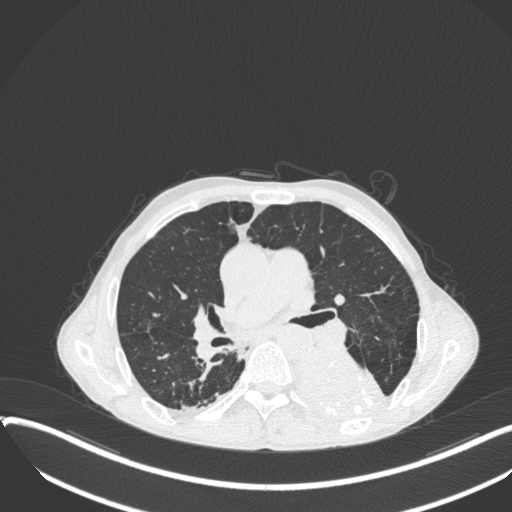
Chest CT, one axial slice; slice 215 of 400 in the series (ordered by position); reconstruction kernel B31f; lung window (W 1500 / L -600 HU); 1 mm slice thickness; 512 × 512 image matrix. Patient: male, 57 years. From the clinical record (not read from this slice): clinical TNM (as recorded): T4 N0 M0.
Structures marked on this image (rectangle marked by the reading radiologist):
- lung tumour (recorded histology: squamous cell carcinoma): bounding box <283,341,389,428> (left, top, right, bottom; pixels)